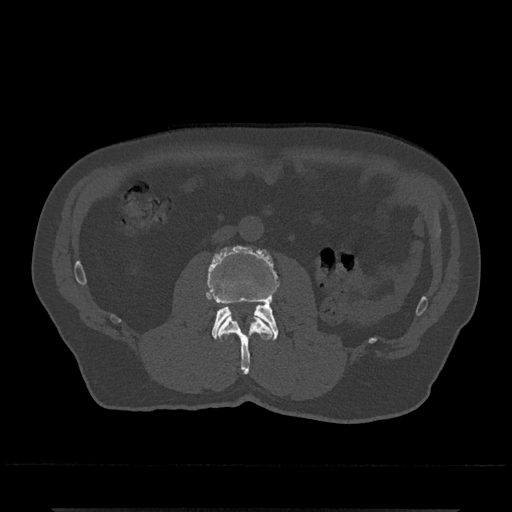
CT including the spine, one axial slice; slice 252 of 797 in the series (ordered by position); bone window (W 1800 / L 400 HU); 0.5 mm slice thickness; 512 × 512 image matrix, field of view 393 × 393 mm. Male patient, age 67 years. Case-level facts recorded for this patient, not image findings: primary cancer: prostate.
Outlined on this slice (semi-automatic segmentation, software-assisted and operator-edited):
- L2 vertebra: bounding box (x1, y1, x2, y2) in pixels: (217, 314, 273, 374)
- L3 vertebra: (206, 246, 279, 341)